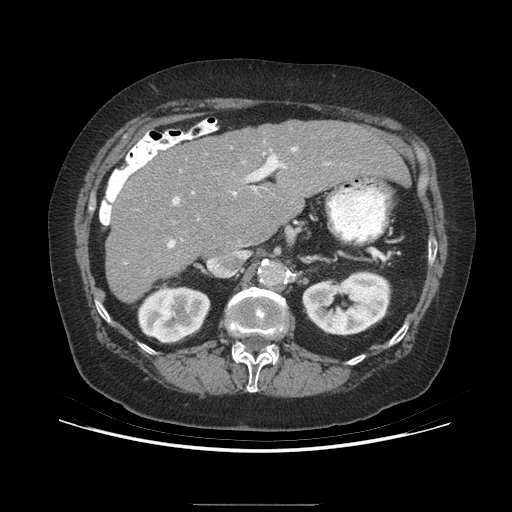
Contrast-enhanced abdominal CT (liver protocol), one axial slice; position 153 of 192 along the scan axis; reconstruction kernel STANDARD; 140 kVp; soft-tissue window (W 400 / L 40 HU); 2.5 mm slice thickness; 512 × 512 image matrix. Case-level facts recorded for this patient, not image findings: diagnosis: hepatocellular carcinoma (patient treated with transarterial chemoembolisation; whether this scan precedes or follows treatment is not stated here); TNM stage (as recorded): Stage-I; Child-Pugh class: A; tumour nodularity: uninodular; tumour size: 3.2 cm.
Structures marked on this image (semi-automatic segmentation, software-assisted and operator-edited):
- liver parenchyma outside the tumour (the mass and vessels are separate outlines, so this box may not span the whole liver): bounding box <106,120,408,302> (left, top, right, bottom; pixels)
- liver vessels: <167,147,330,248>